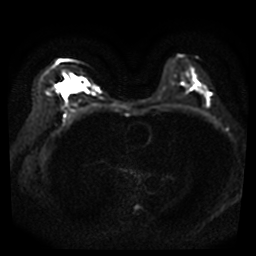
Breast MRI, one axial slice; position 23 of 40 along the scan axis; diffusion-weighted series; image 2 of 4 stored at this slice position (different b-values; order by instance number); 3 T; 256 × 256 image matrix. Female patient.
Structures marked on this image (expert manual segmentation):
- tumour on diffusion-weighted imaging: bounding box <58,80,87,95> (left, top, right, bottom; pixels)